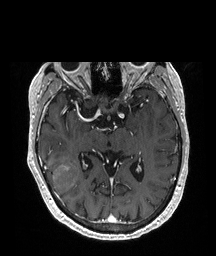
Brain MRI from a brain-tumour surgery series, one axial slice; position 119 of 208 along the scan axis; T1-weighted post-contrast; 1 mm slice thickness; 216 × 256 image matrix. From the clinical record (not read from this slice): histopathology: Glioblastoma; WHO grade: 4; IDH mutation: no.
Structures marked on this image (expert manual segmentation):
- tumour: bounding box <40,152,77,194> (left, top, right, bottom; pixels)